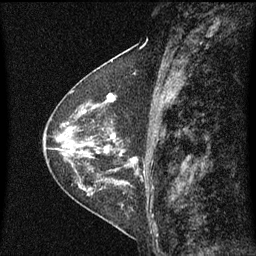
Breast MRI (dynamic contrast-enhanced), one sagittal slice. Position 29 of 60 along the scan axis. Dynamic contrast-enhanced series, image 2 of 3 at this slice position (ordered by acquisition). 1.5 T. TE 4.2 ms, TR 8 ms. 2 mm slice thickness. 256 × 256 image matrix, field of view 200 × 200 mm. Female patient, age 48 years.
Outlined on this slice (semi-automatically segmented with operator editing):
- analysis volume of interest (the breast-tissue region the enhancement analysis was run in; not a lesion): bounding box (x1, y1, x2, y2) in pixels: (103, 74, 145, 139)
- tumour enhancement mask (voxels above the 70 % enhancement threshold inside the analysis volume of interest): (106, 92, 115, 139)